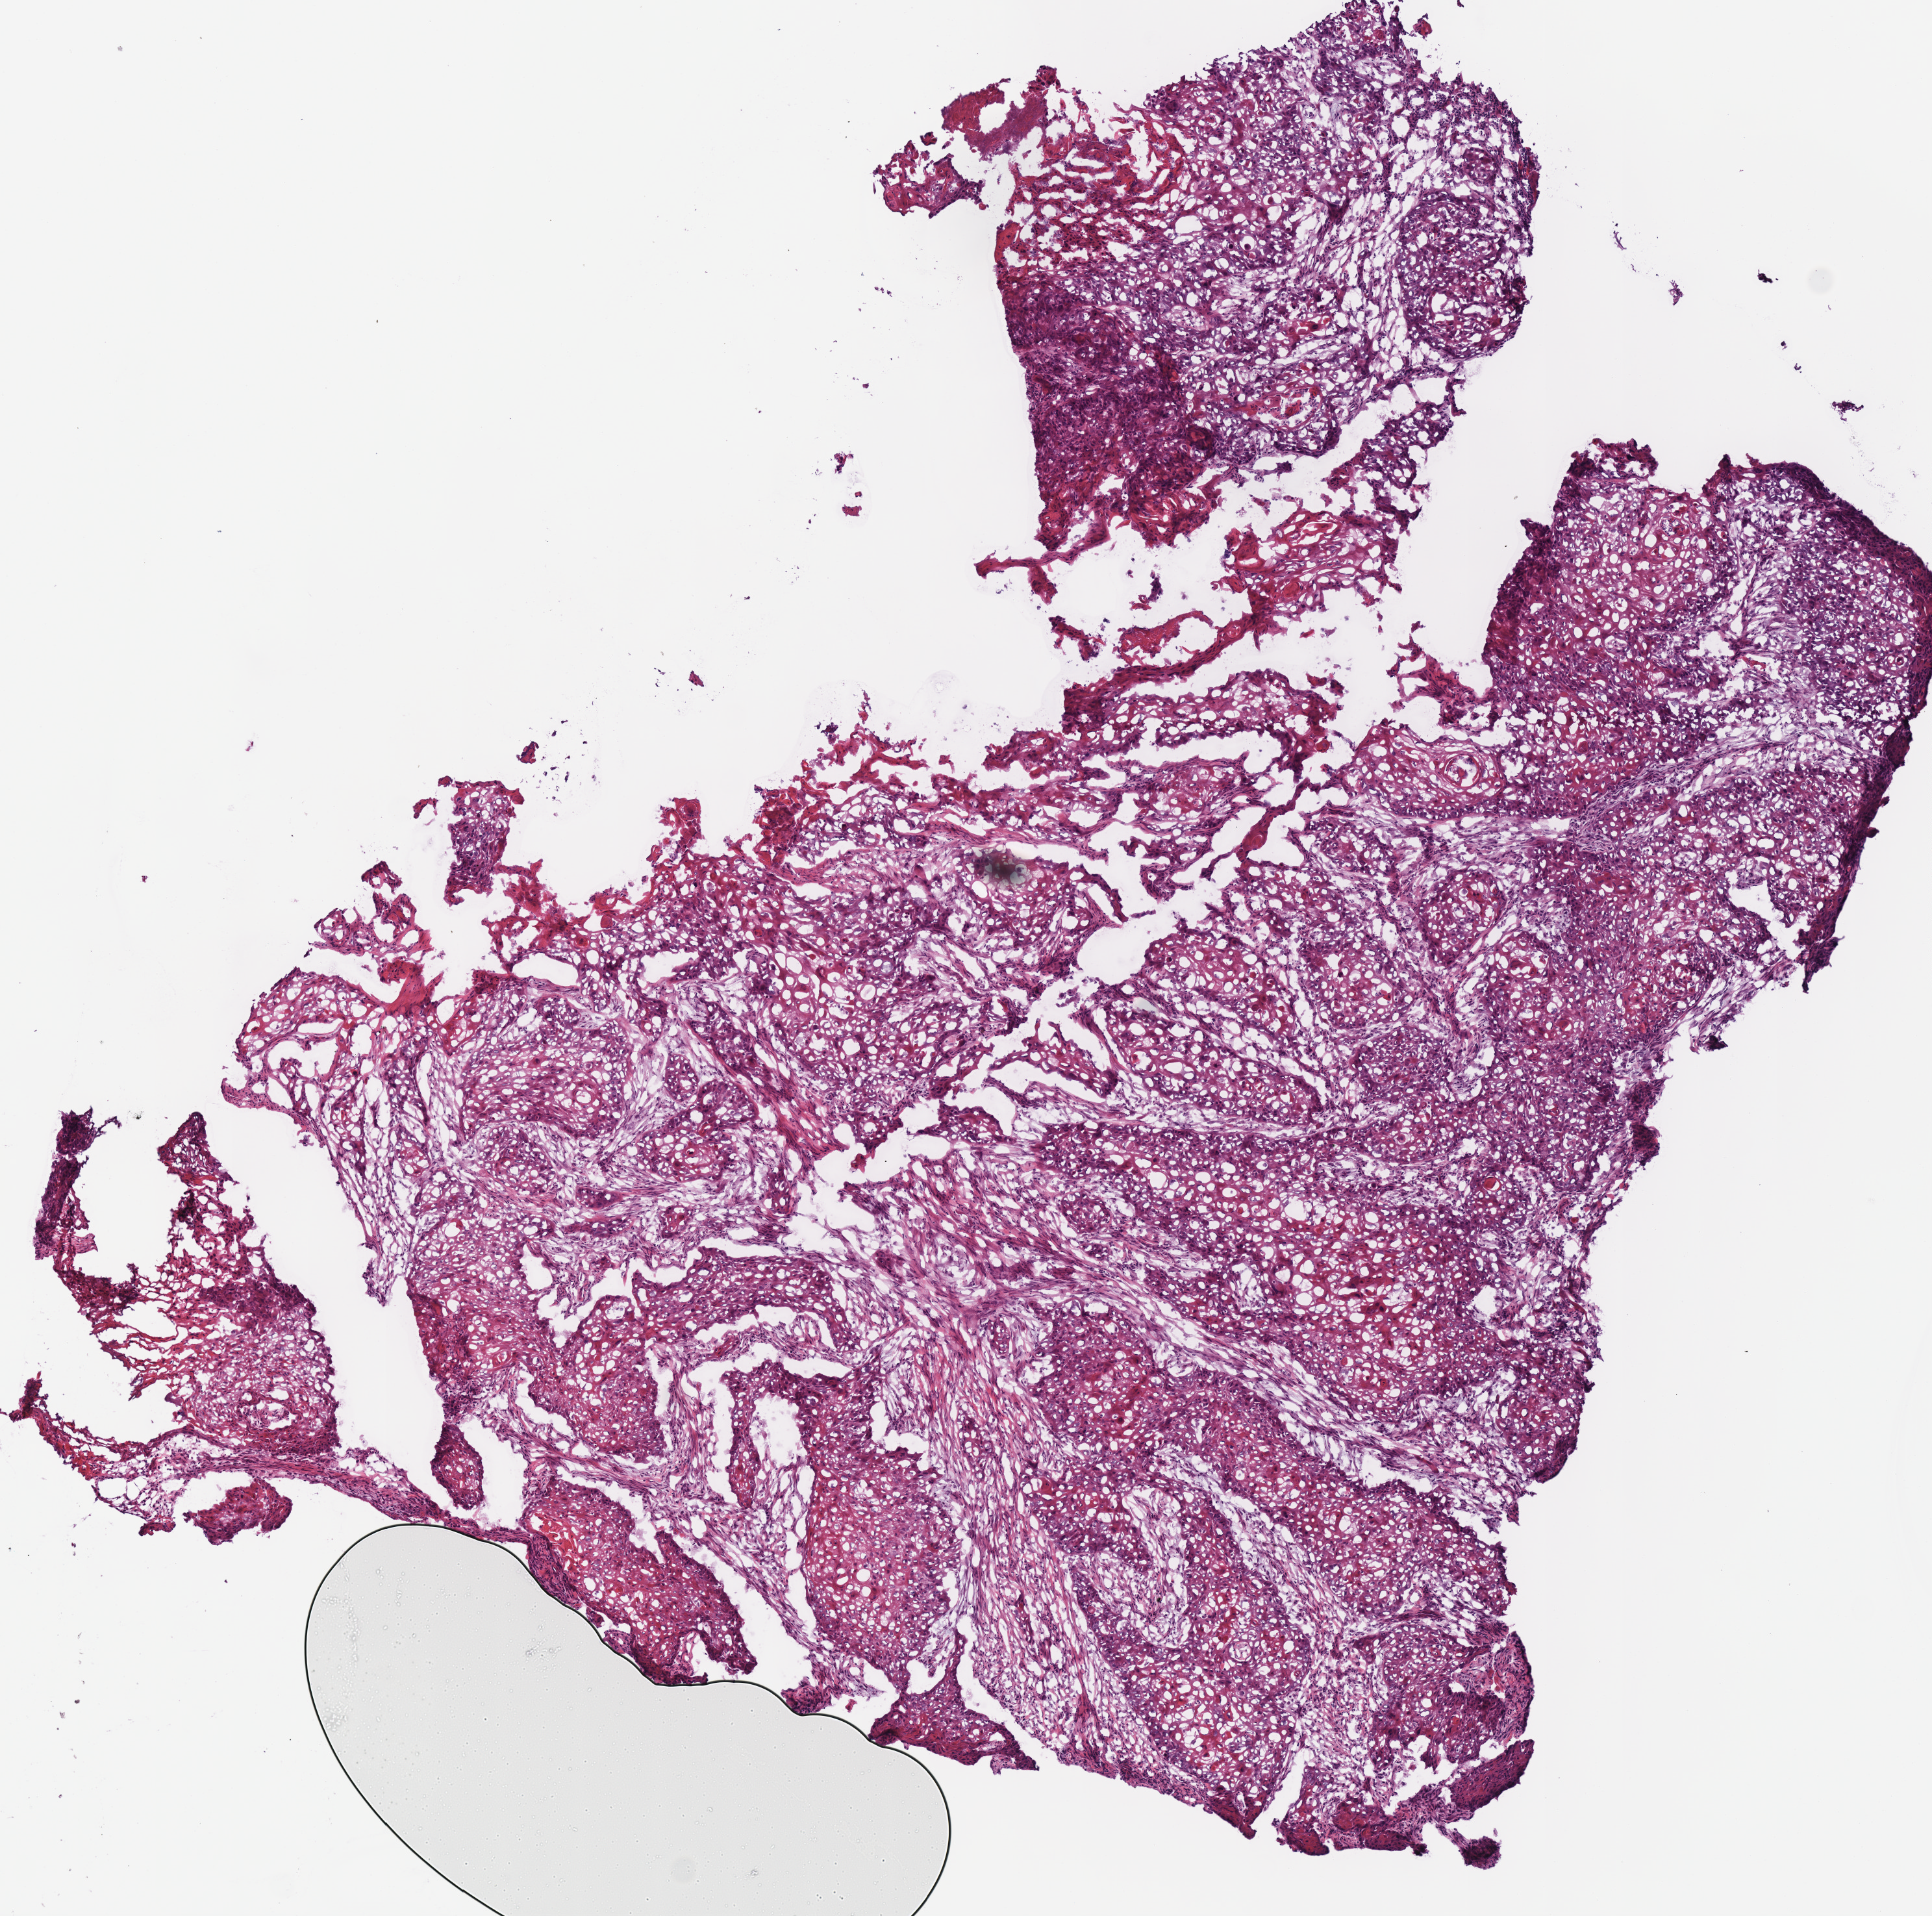
Whole-slide histology image, Hematoxylin and eosin (H&E) stained — shown as a low-resolution overview of the whole scanned area (about 5.9 x 5.8 mm, from a 40x scan). Frozen section from the bottom of the tissue portion. Primary tumour sample from the head and neck. Male, age 79 years at initial diagnosis. Histologic grade: G1 (well differentiated). Composition of this section per pathologist review: tumour cells 85%, tumour nuclei 80%, normal cells 0%, stromal cells 15%, necrosis 0%.
Pathologic diagnosis: Squamous cell carcinoma, NOS (overlapping lesion of lip, oral cavity and pharynx). AJCC pathologic stage: II (7th edition). Laterality: left.